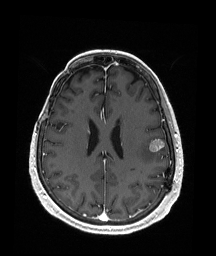
Brain MRI from a brain-tumour surgery series, one axial slice; slice 73 of 176 in the series (ordered by position); T1-weighted post-contrast; 1 mm slice thickness; 216 × 256 image matrix, field of view 211 × 250 mm. Case-level facts recorded for this patient, not image findings: histopathology: Metastatic Malignant Melanoma; tumour location: Left Frontal.
Annotated regions visible in this slice (manually delineated by an expert):
- tumour: box from (x=148, y=138) to (x=165, y=152) px